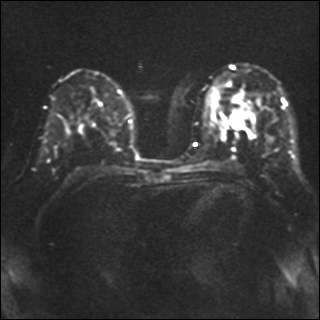
Breast MRI, one axial slice; slice 19 of 40 in the series (ordered by position); diffusion-weighted series; image 2 of 4 stored at this slice position (different b-values; order by instance number); 1.5 T; 4 mm slice thickness; 320 × 320 image matrix, field of view 320 × 320 mm. Female patient.
Outlined on this slice (manually delineated by an expert):
- tumour on diffusion-weighted imaging: box from (x=231, y=104) to (x=251, y=128) px